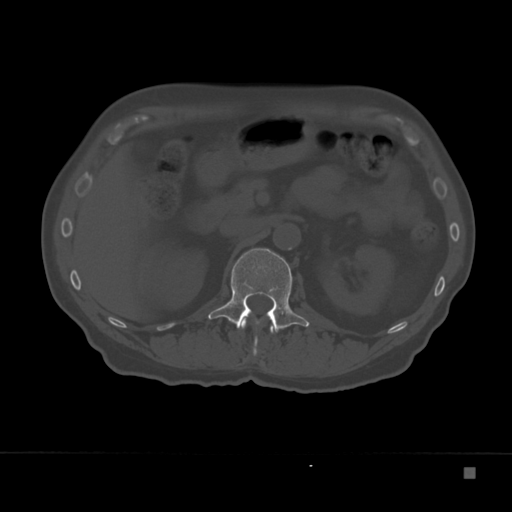
CT including the spine, one axial slice. Slice 114 of 332 in the series (ordered by position). Bone window (W 1800 / L 400 HU). 1.5 mm slice thickness. 512 × 512 image matrix. Patient: male, 72 years. From the clinical record (not read from this slice): primary cancer: skeletal.
Outlined on this slice (semi-automatic segmentation, software-assisted and operator-edited):
- L1 vertebra: box from (x=208, y=248) to (x=310, y=355) px
- T12 vertebra: (x=241, y=318)–(x=274, y=334)